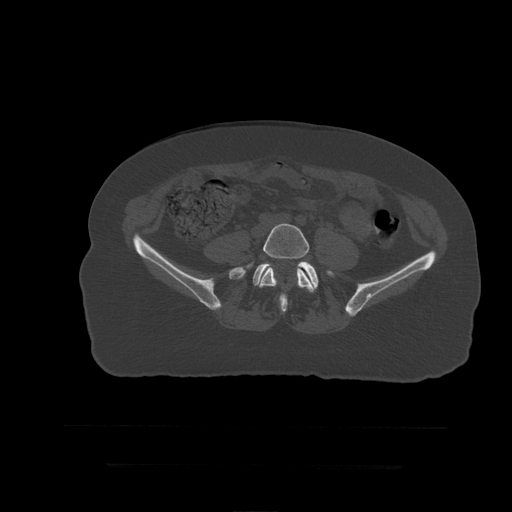
CT including the spine, one axial slice; slice 67 of 399 in the series (ordered by position); reconstruction kernel STANDARD; 120 kVp; bone window (W 1800 / L 400 HU); 1.25 mm slice thickness; 512 × 512 image matrix. Patient age 41 years. Case-level facts recorded for this patient, not image findings: primary cancer: breast.
Structures marked on this image (semi-automatically segmented with operator editing):
- L5 vertebra: bounding box (x1, y1, x2, y2) in pixels: (247, 224, 315, 299)